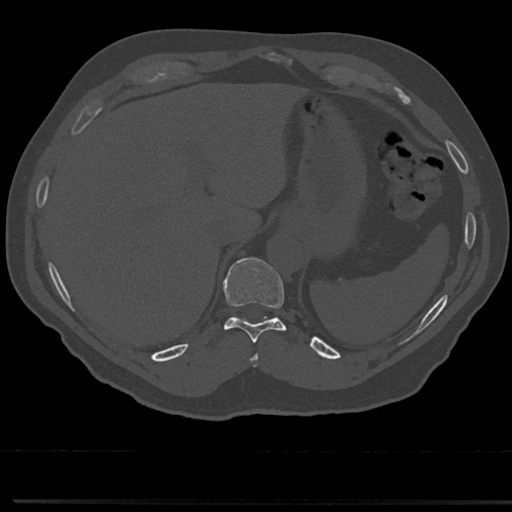
CT including the spine, one axial slice. Slice 251 of 817 in the series (ordered by position). 120 kVp. Bone window (W 1800 / L 400 HU). 0.5 mm slice thickness. 512 × 512 image matrix, field of view 355 × 355 mm. Male patient, age 61 years. Case-level facts recorded for this patient, not image findings: primary cancer: prostate.
Annotated regions visible in this slice (semi-automatic segmentation, software-assisted and operator-edited):
- T10 vertebra: bounding box [x1, y1, x2, y2] px = [213, 258, 296, 344]
- T9 vertebra: [250, 349, 260, 368]